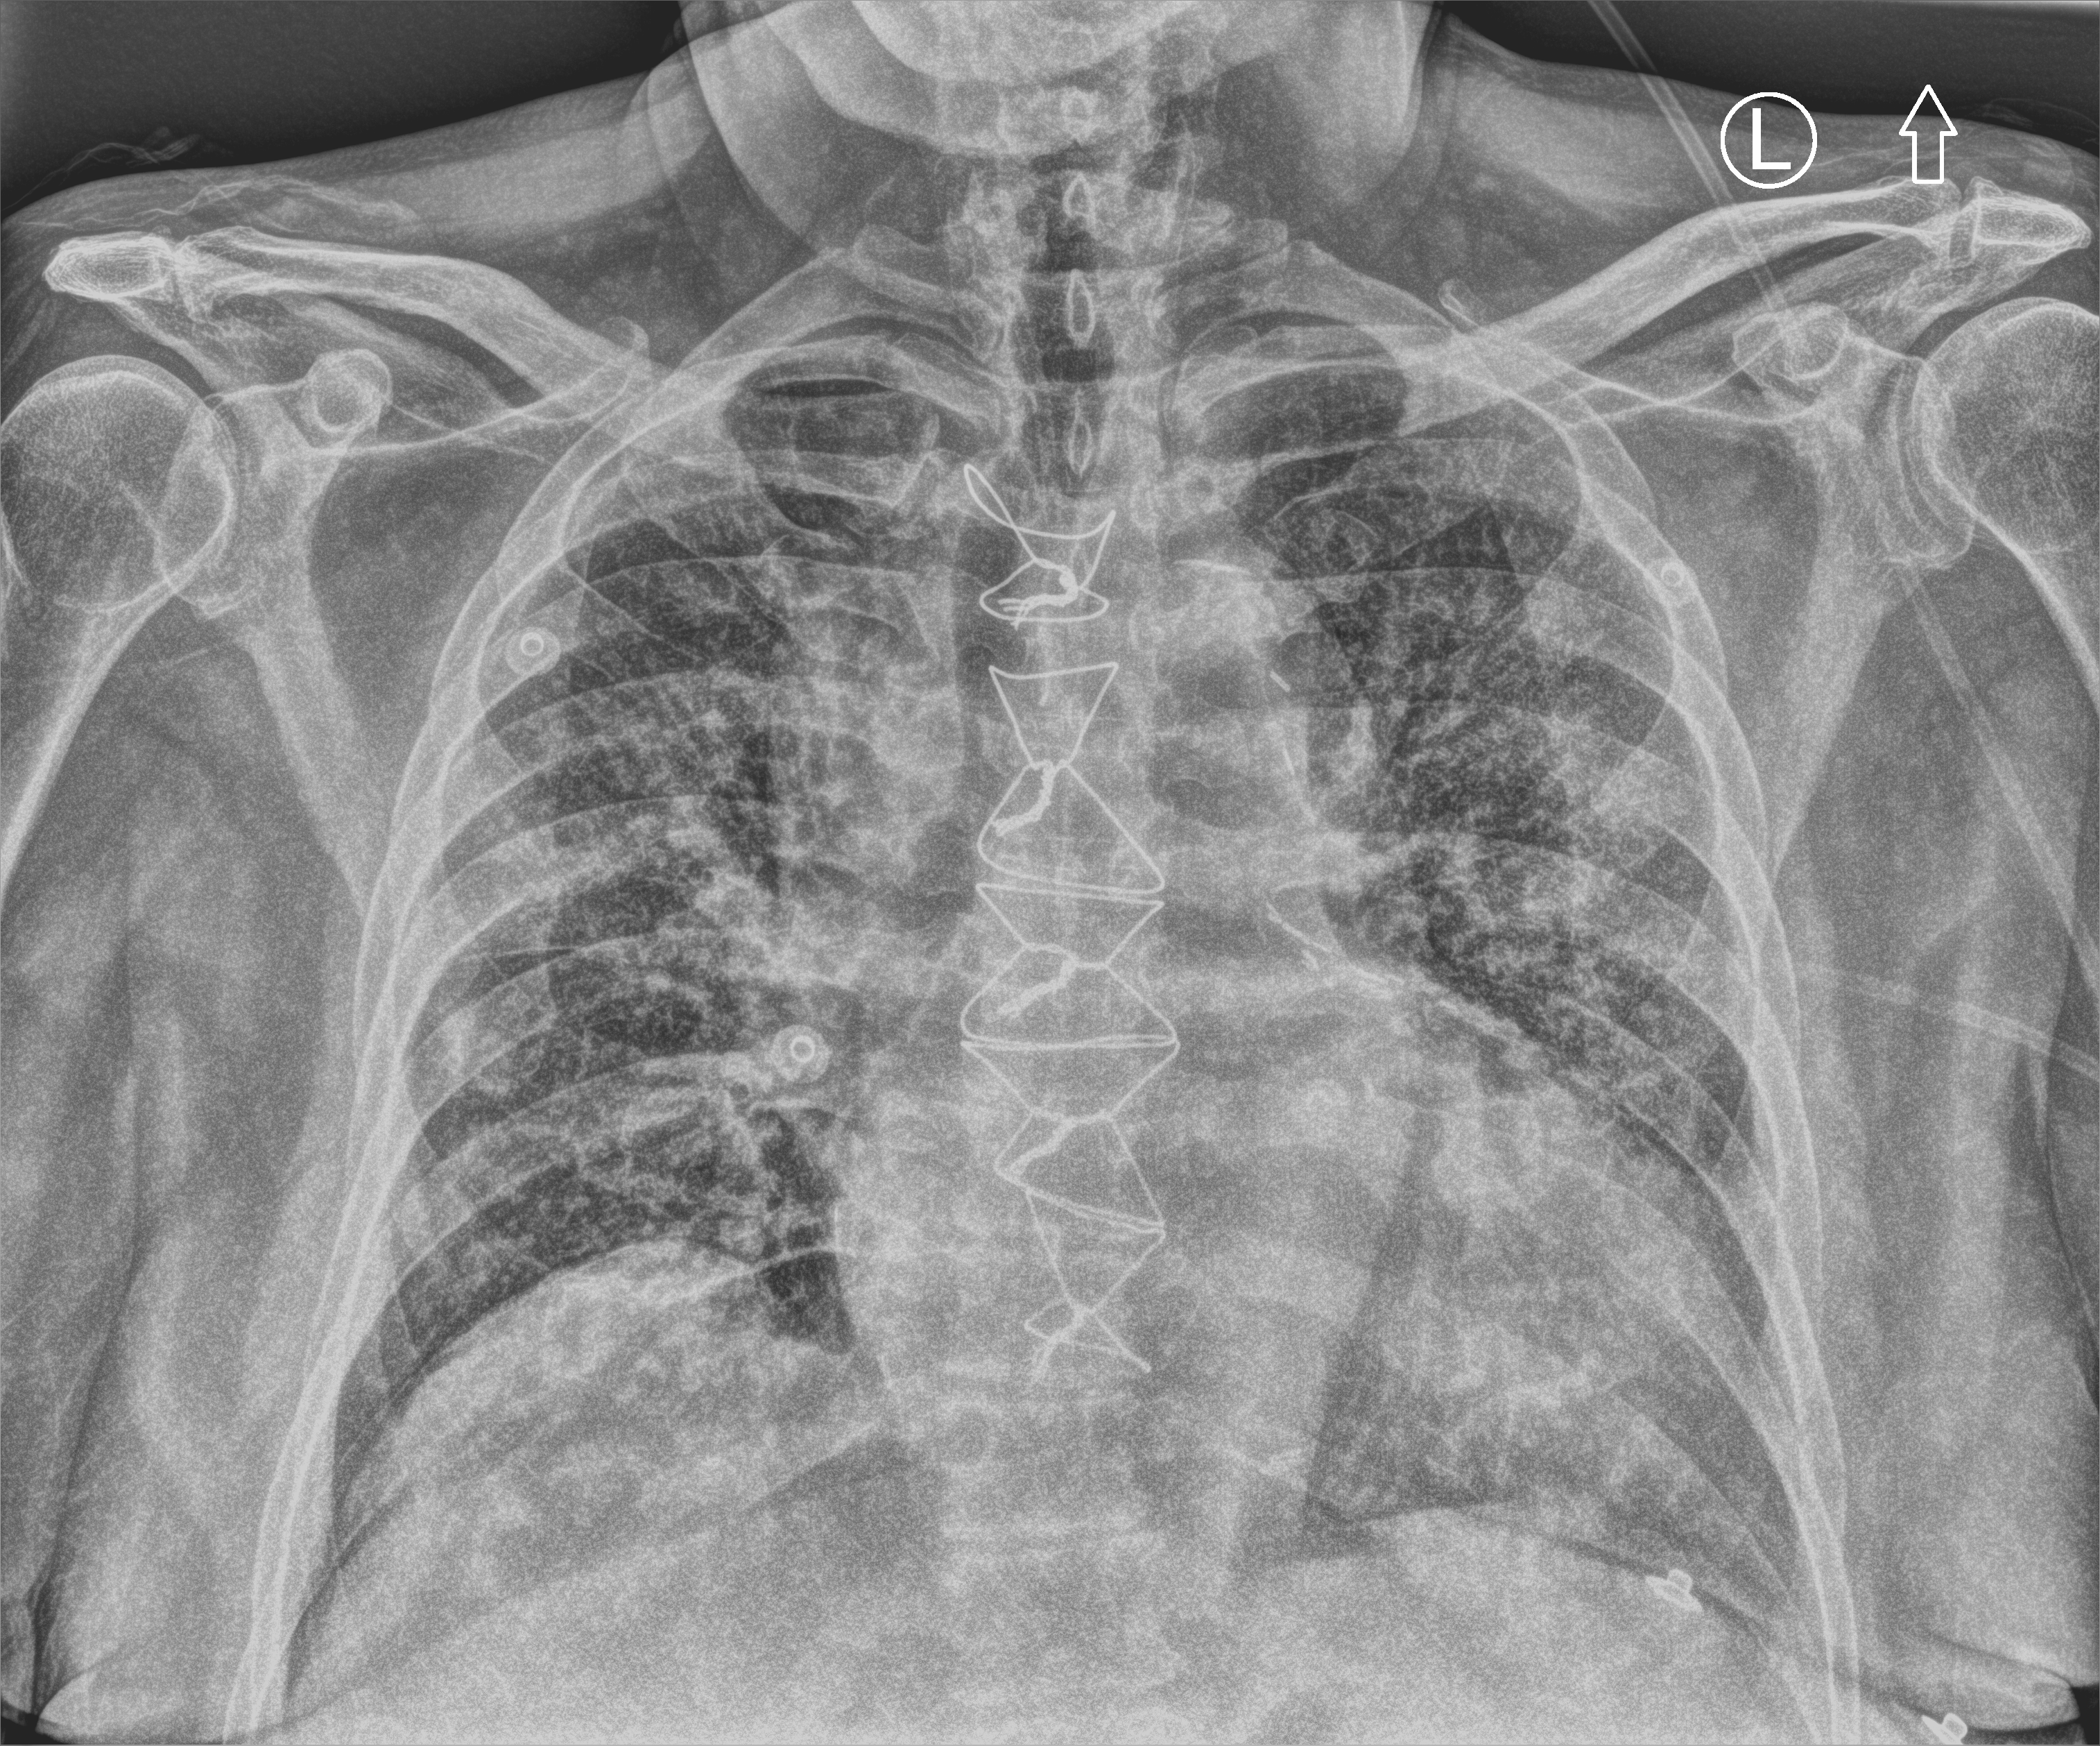
Bedside chest radiograph (computed radiography). Male patient hospitalised with COVID-19, age 75–90 years.
Admission-level facts for this patient (not findings on this image; timing relative to this image not recorded):
- length of hospital stay: 28 days